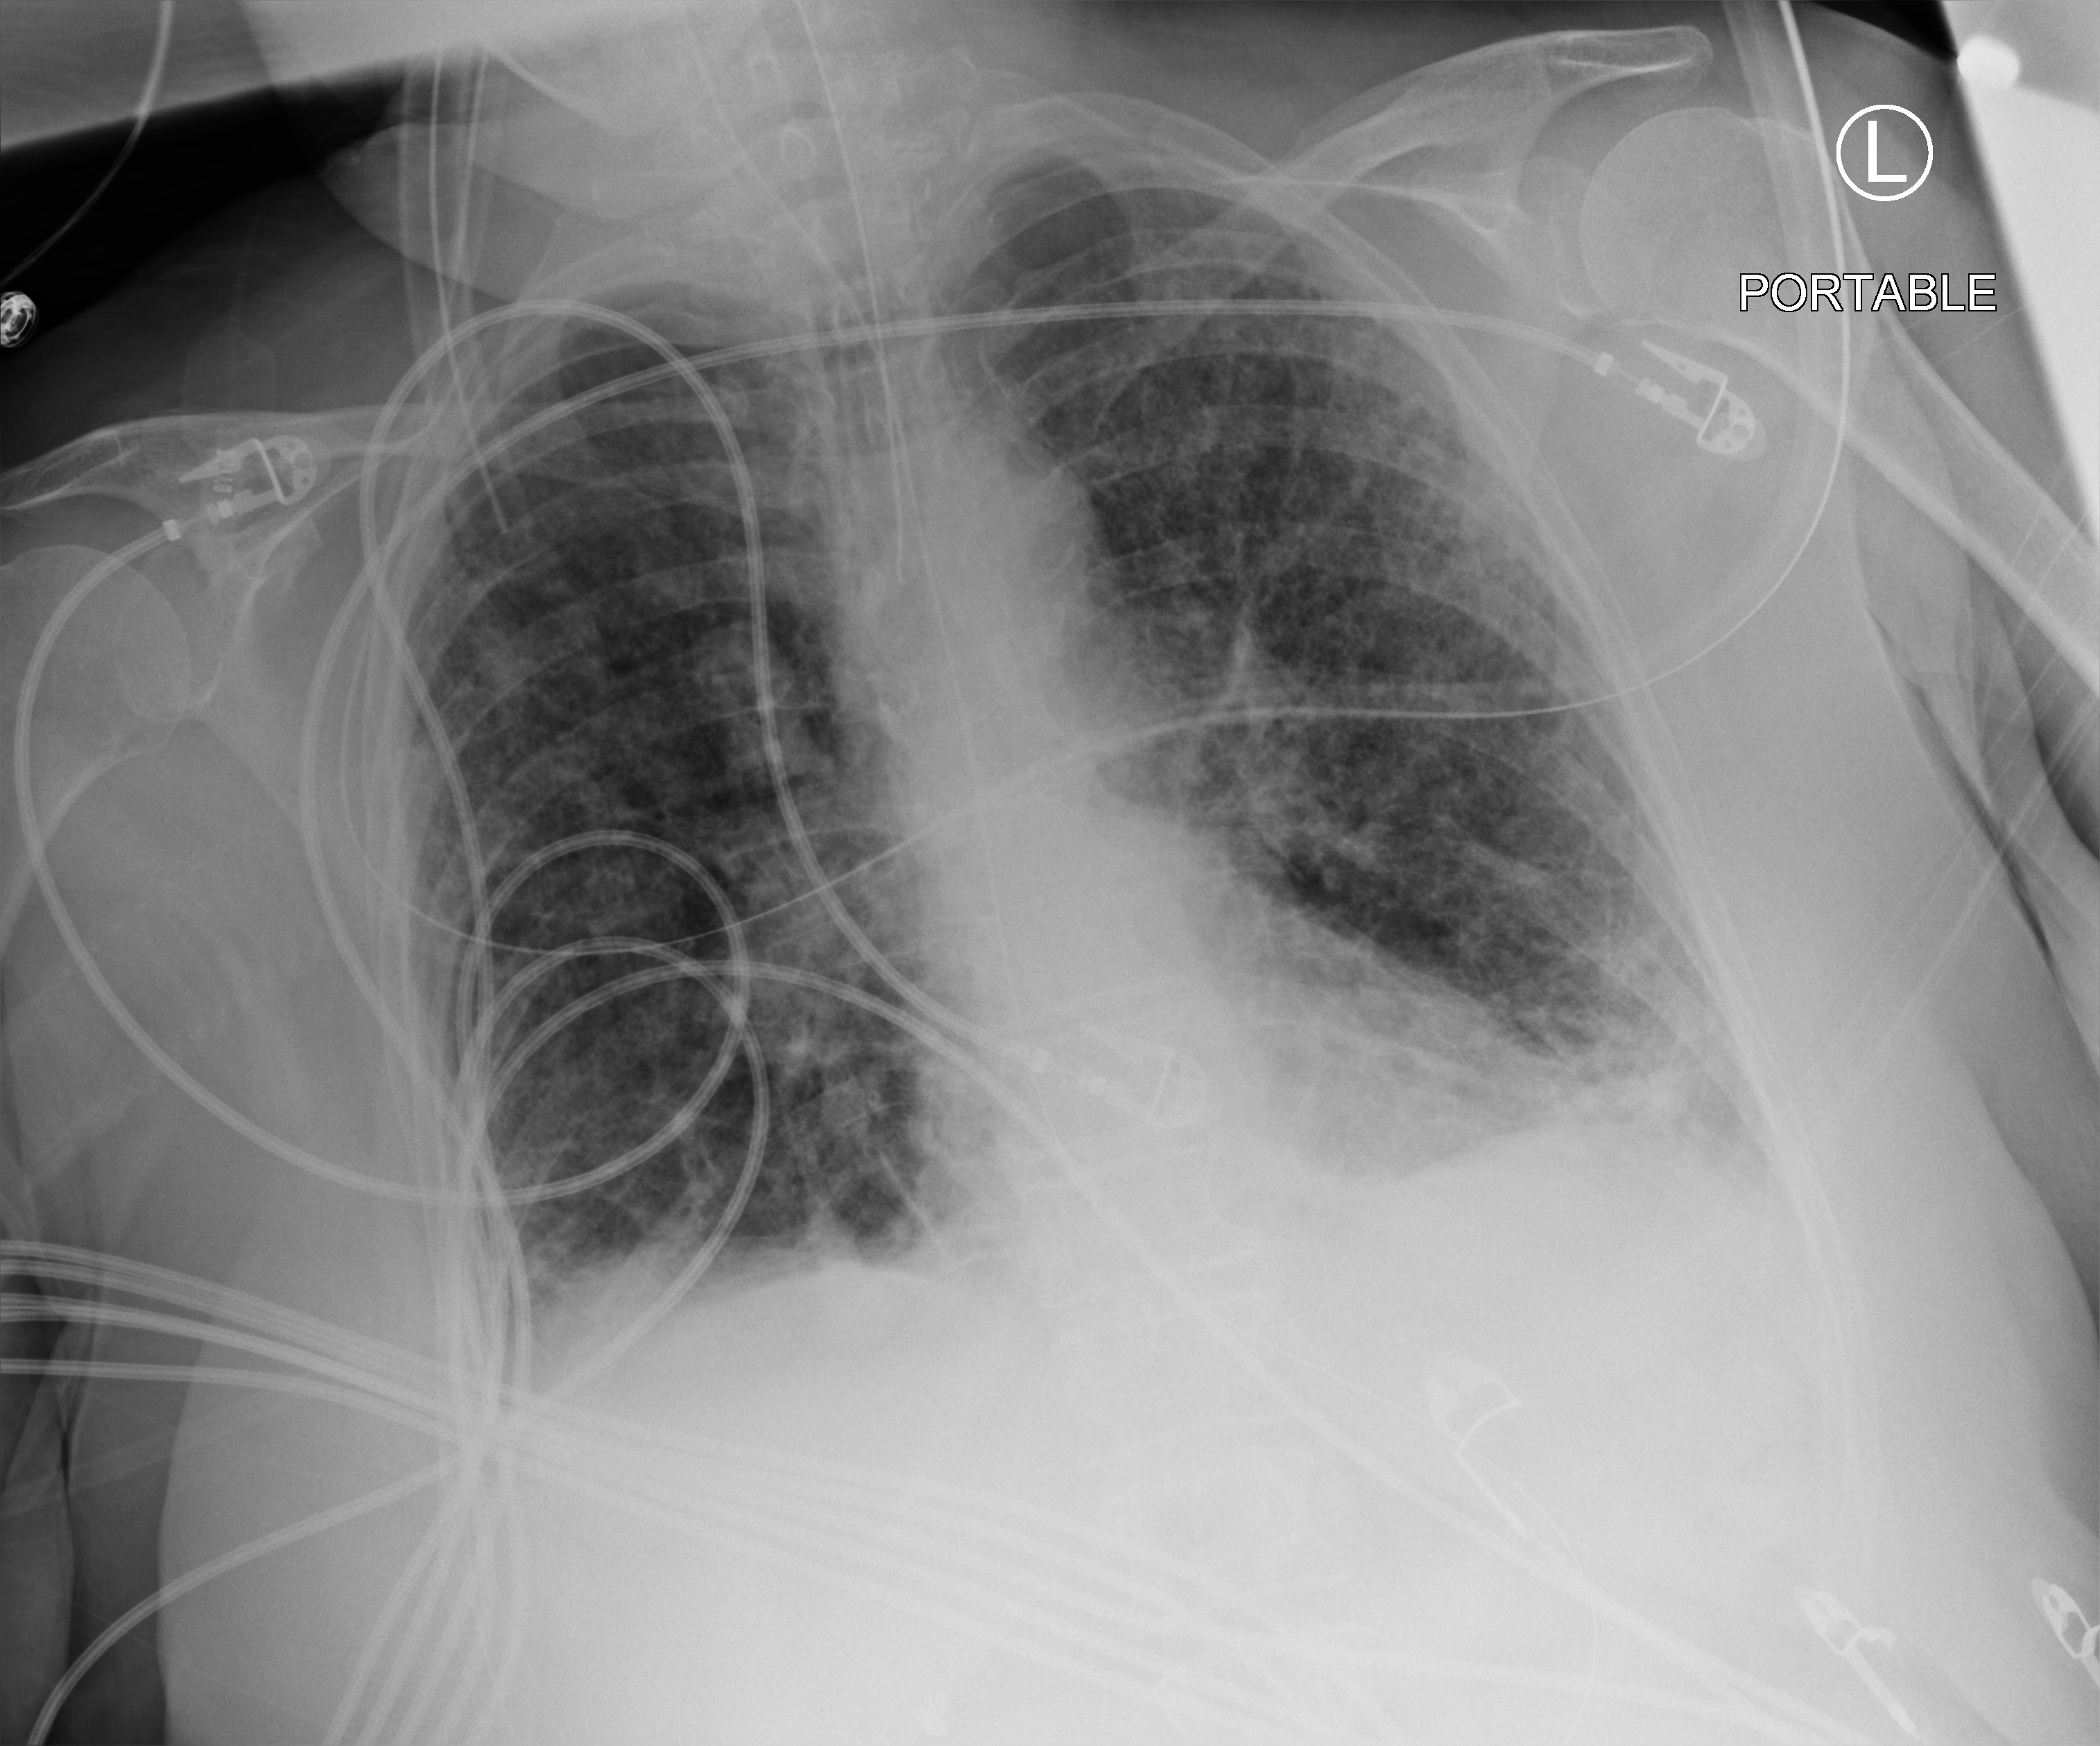
Chest X-ray (portable); anteroposterior (AP) projection. Female patient hospitalised with COVID-19, age 60–74 years.
Admission-level facts for this patient (not findings on this image; timing relative to this image not recorded): mechanically ventilated during this hospital stay: yes; admitted to intensive care during this hospital stay: yes.